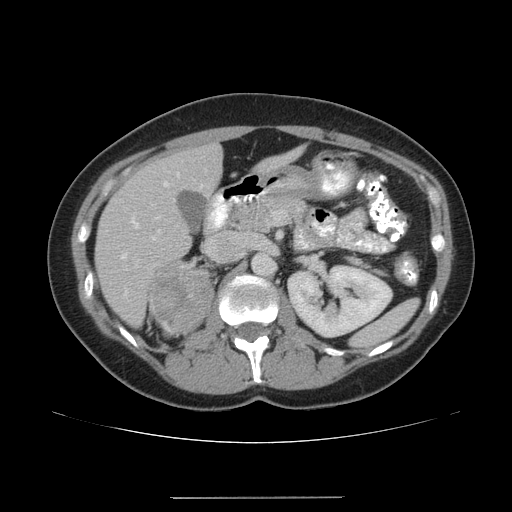
Contrast-enhanced abdominal CT, one axial slice; position 102 of 161 along the scan axis; intravenous contrast given; soft-tissue window (W 400 / L 40 HU); 3.75 mm slice thickness; 512 × 512 image matrix. Female patient. Case-level facts recorded for this patient, not image findings: diagnosis: adrenocortical carcinoma; tumour side: right adrenal; tumour size at pathology: 9 cm; Ki-67 index: 14 %; stage (as recorded): 3.
Outlined on this slice (semi-automatically segmented with operator editing):
- mass: bounding box (x1, y1, x2, y2) in pixels: (152, 264, 211, 335)